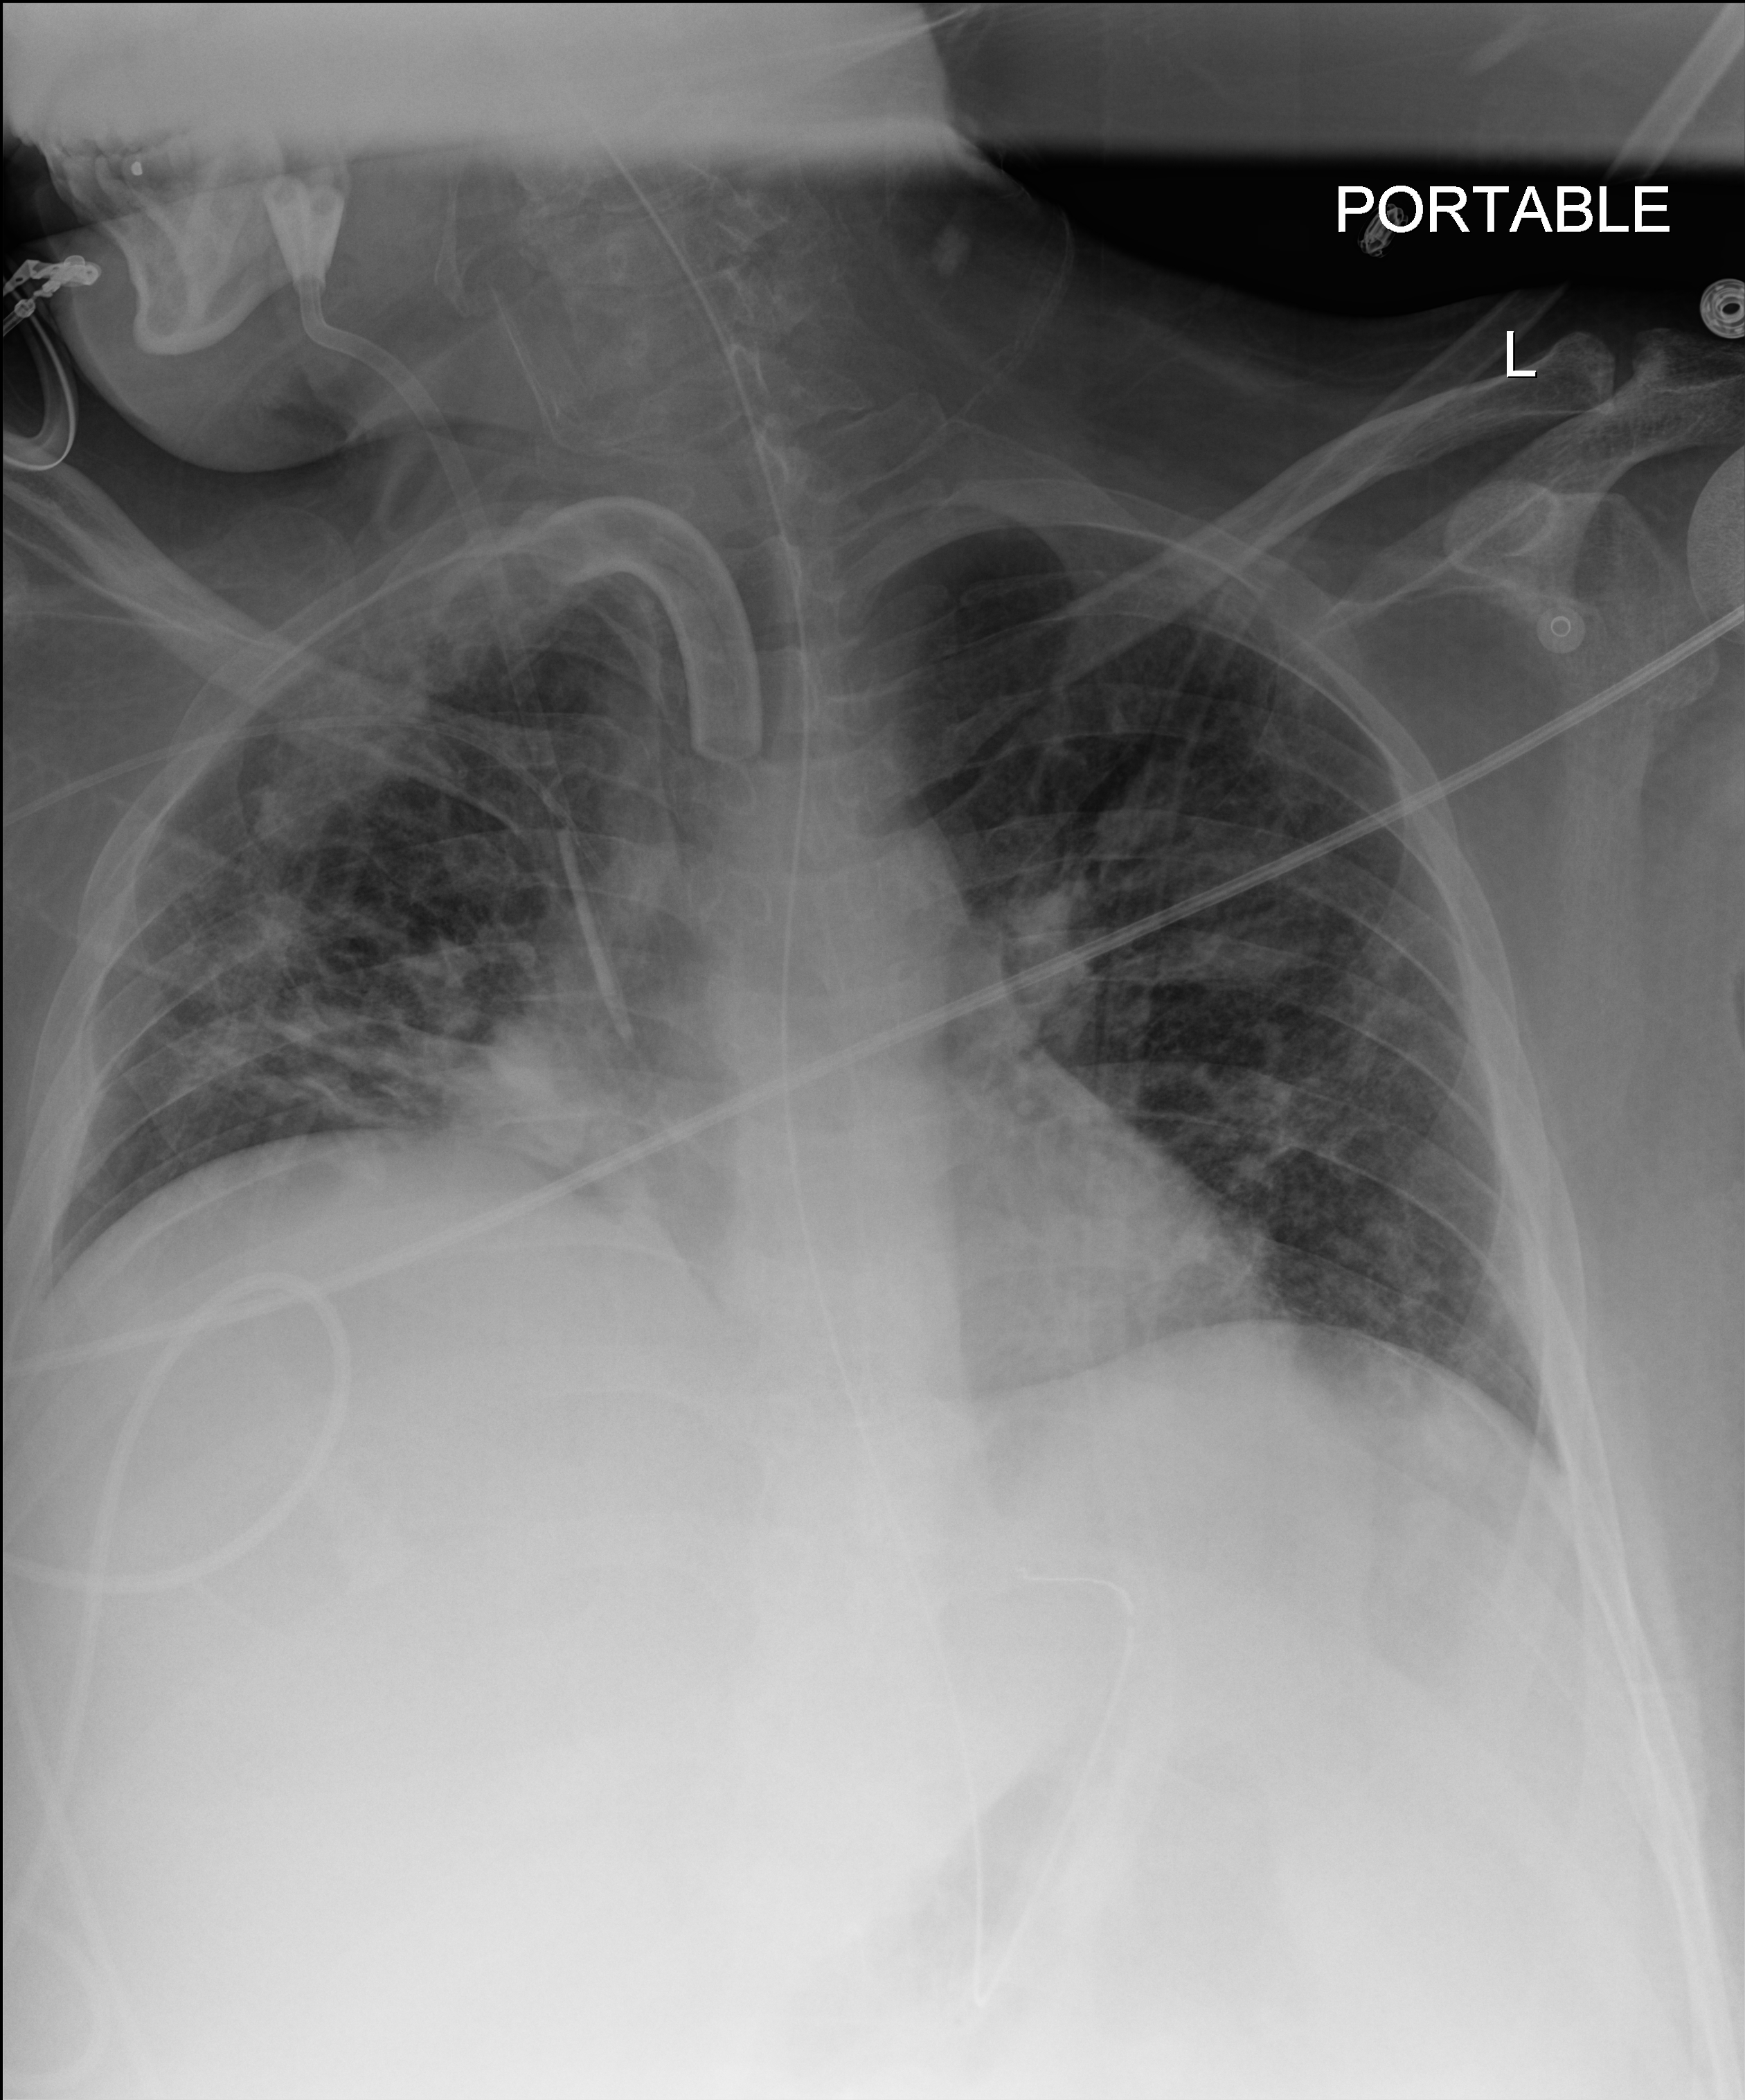
Bedside chest radiograph (digital radiography), anteroposterior (AP) projection. Patient hospitalised with COVID-19, aged 18–59 years.
Admission-level facts for this patient (not findings on this image; timing relative to this image not recorded):
- mechanically ventilated during this hospital stay: yes
- other chronic lung disease (admission record): yes